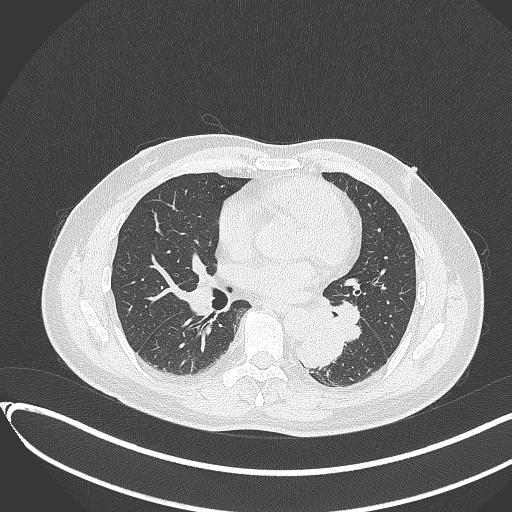
Chest CT, one axial slice. 120 kVp. Lung window (W 1500 / L -600 HU). 512 × 512 image matrix, field of view 400 × 400 mm. Patient: male, 54 years. Case-level facts recorded for this patient, not image findings: clinical TNM (as recorded): T3 N0 M0.
Outlined on this slice (rectangle marked by the reading radiologist):
- lung tumour (recorded histology: squamous cell carcinoma): bounding box [x1, y1, x2, y2] px = [292, 327, 346, 368]